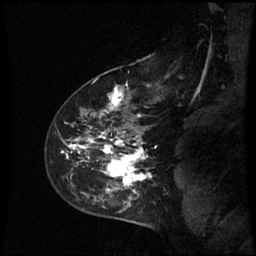
Breast MRI (dynamic contrast-enhanced), one sagittal slice. Slice 44 of 60 in the series (ordered by position). Dynamic contrast-enhanced series, image 2 of 3 at this slice position (ordered by acquisition). 1.5 T. TE 4.2 ms, TR 8.9 ms. 256 × 256 image matrix, field of view 210 × 210 mm. Female patient, age 43 years. Case-level facts recorded for this patient, not image findings: setting: breast cancer imaged before/during neoadjuvant chemotherapy; receptor status: HER2-positive.
Annotated regions visible in this slice (semi-automatic segmentation, software-assisted and operator-edited):
- analysis volume of interest (the breast-tissue region the enhancement analysis was run in; not a lesion): box from (x=56, y=80) to (x=161, y=195) px
- tumour enhancement mask (voxels above the 70 % enhancement threshold inside the analysis volume of interest): (x=63, y=87)–(x=152, y=193)